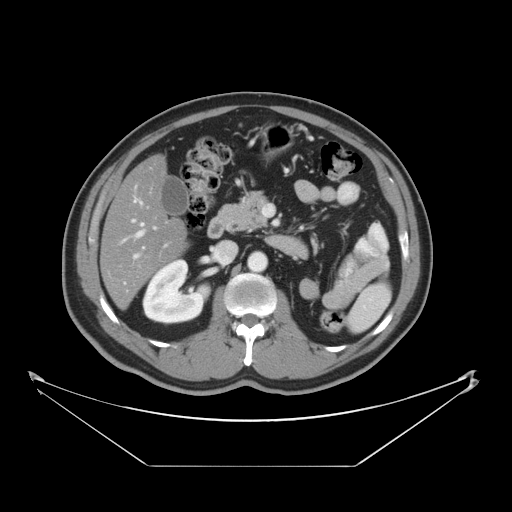
Contrast-enhanced abdominal CT, one axial slice. Position 20 of 46 along the scan axis. Reconstruction kernel STANDARD. 120 kVp. Soft-tissue window (W 400 / L 40 HU). 5 mm slice thickness. 512 × 512 image matrix, field of view 465 × 465 mm. Male patient, age 57 years. From the clinical record (not read from this slice): diagnosis: colorectal cancer liver metastases, imaged before liver resection; multiple liver metastases: no.
Outlined on this slice (manually delineated by an expert):
- hepatic veins: bounding box <132,219,144,237> (left, top, right, bottom; pixels)
- liver: <103,156,187,307>
- planned liver remnant (the part of the liver to remain after resection): <103,156,187,307>
- portal vein (with intrahepatic branches): <134,247,144,258>